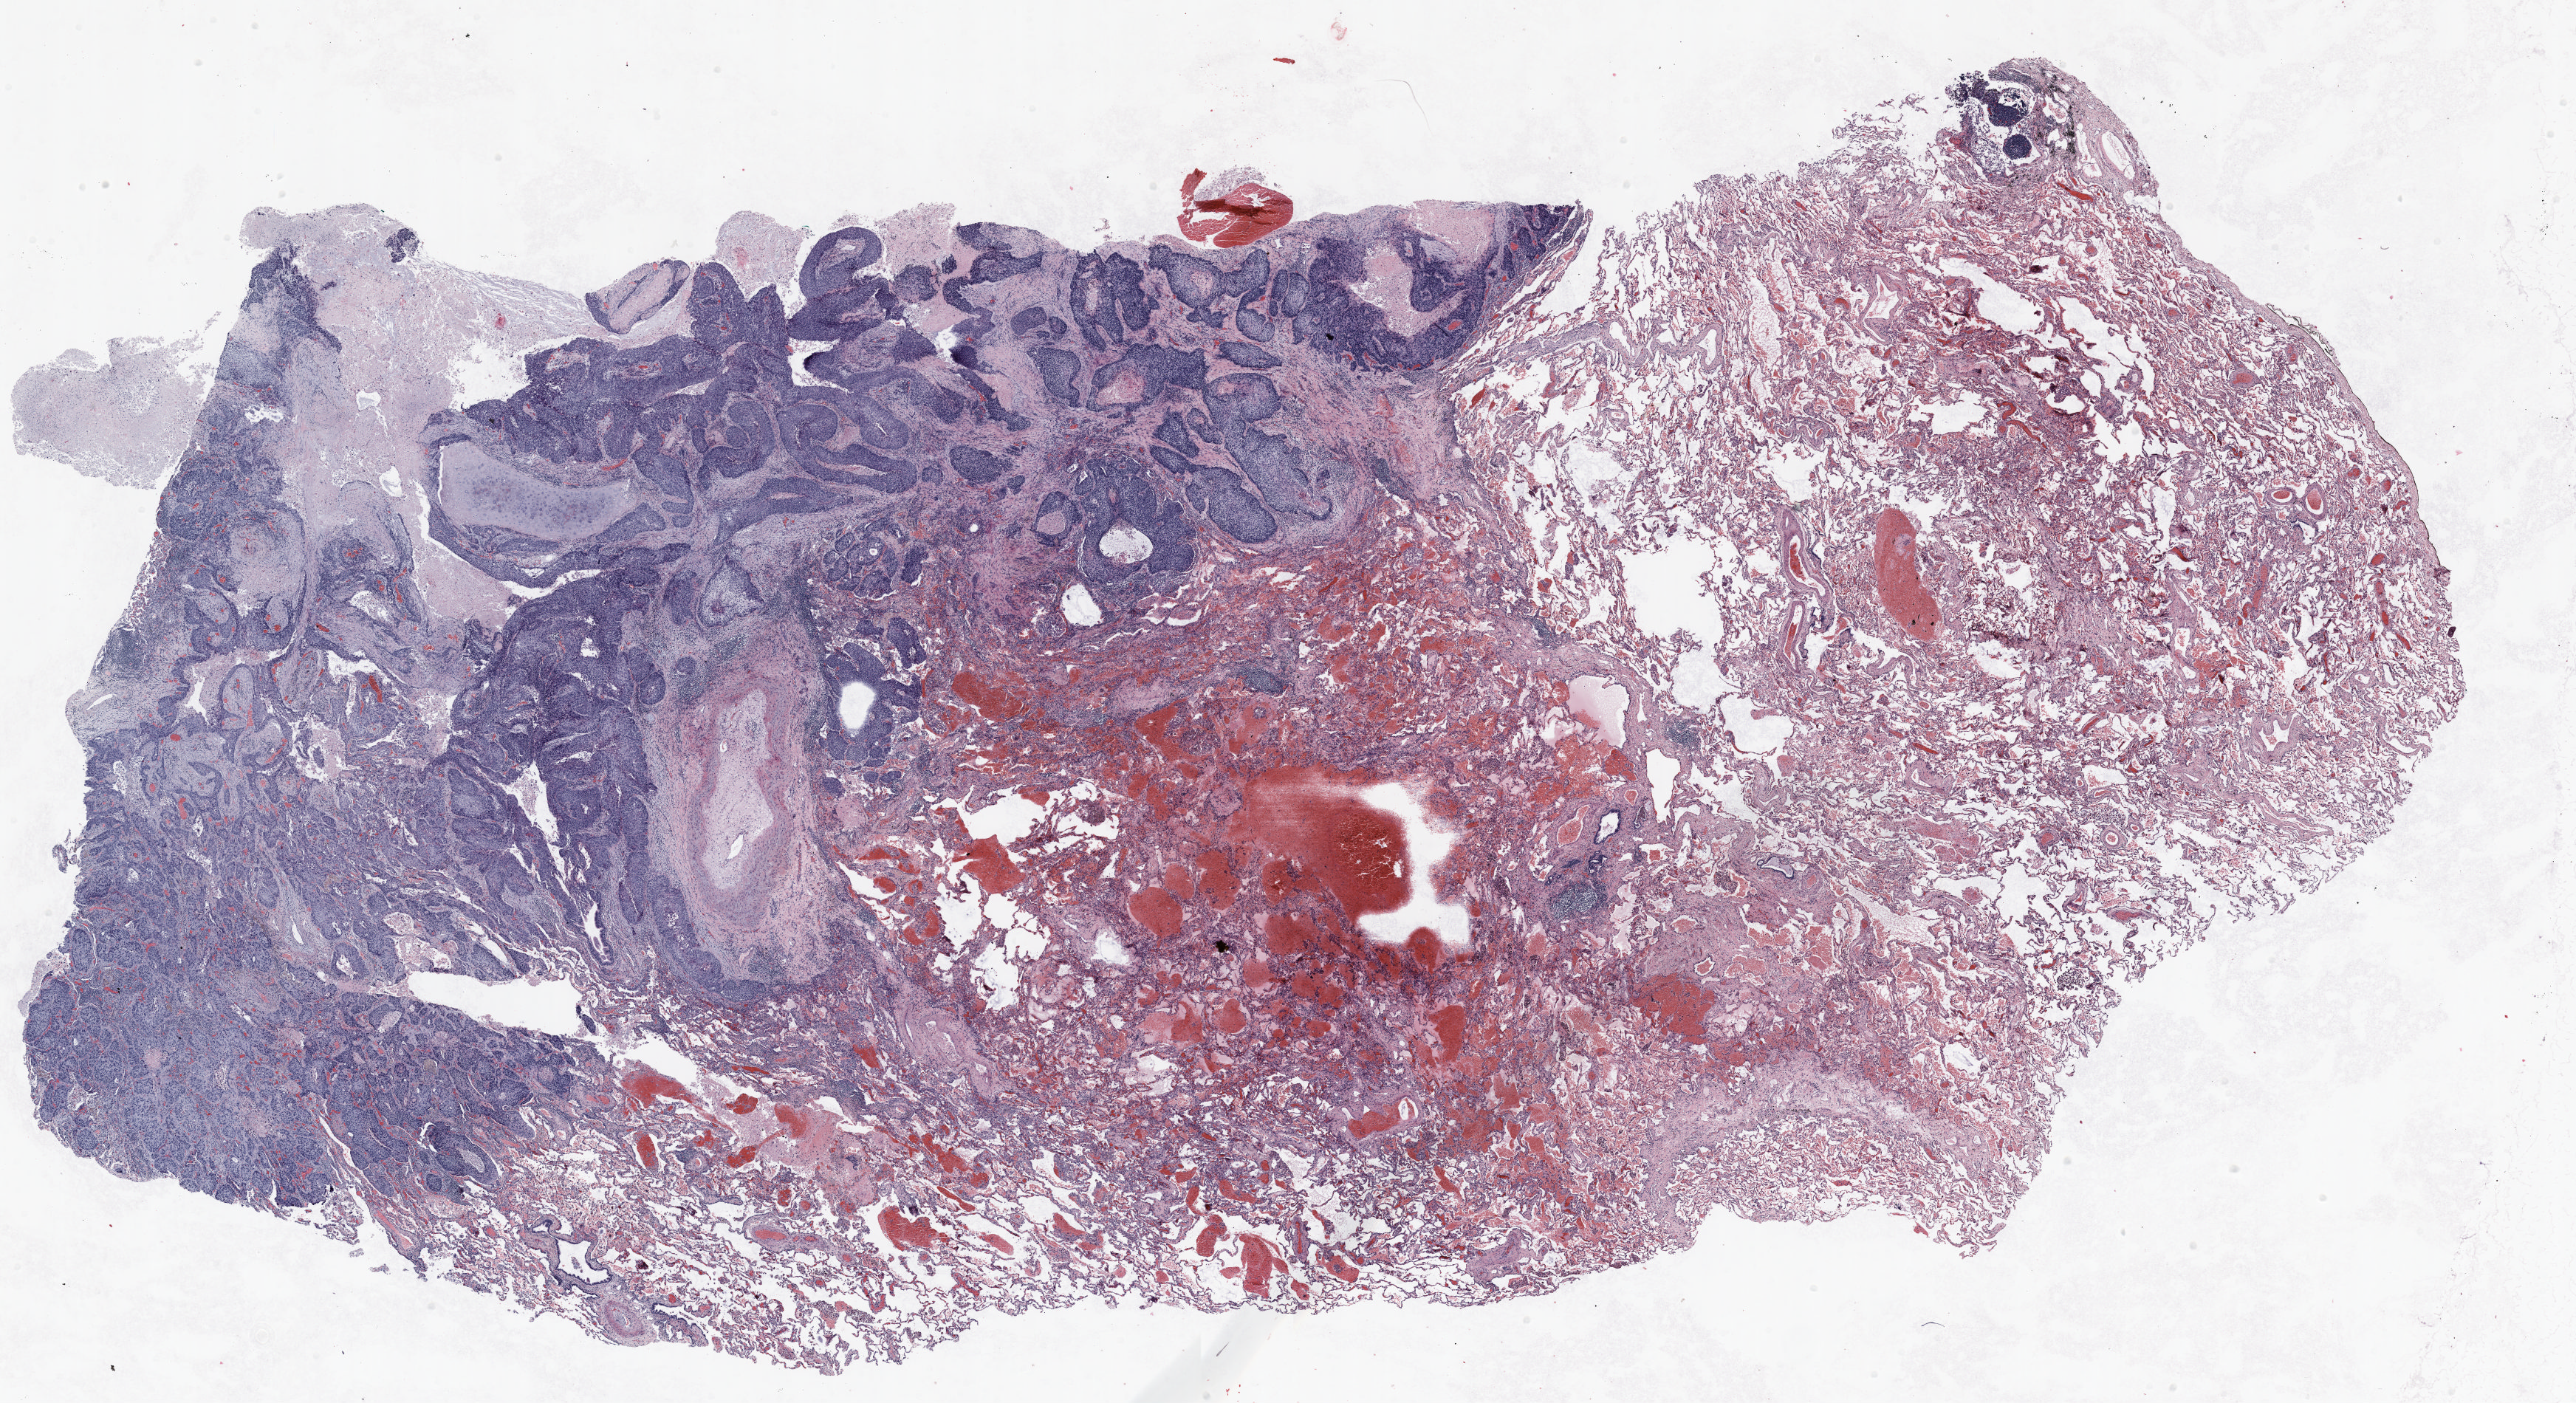
H&E whole-slide image — a low-resolution overview of the entire scanned area, about 28.0 x 15.3 mm; formalin-fixed paraffin-embedded (FFPE) section; lung tissue. Female patient, aged 58 at enrolment. Grade: moderately differentiated (G2).
- stage (AJCC 6th edition): IA
- participant's lung-cancer diagnosis: Squamous cell carcinoma, NOS
- primary tumour location (clinical record): right upper lobe
- tumour size (pathology): 17 mm